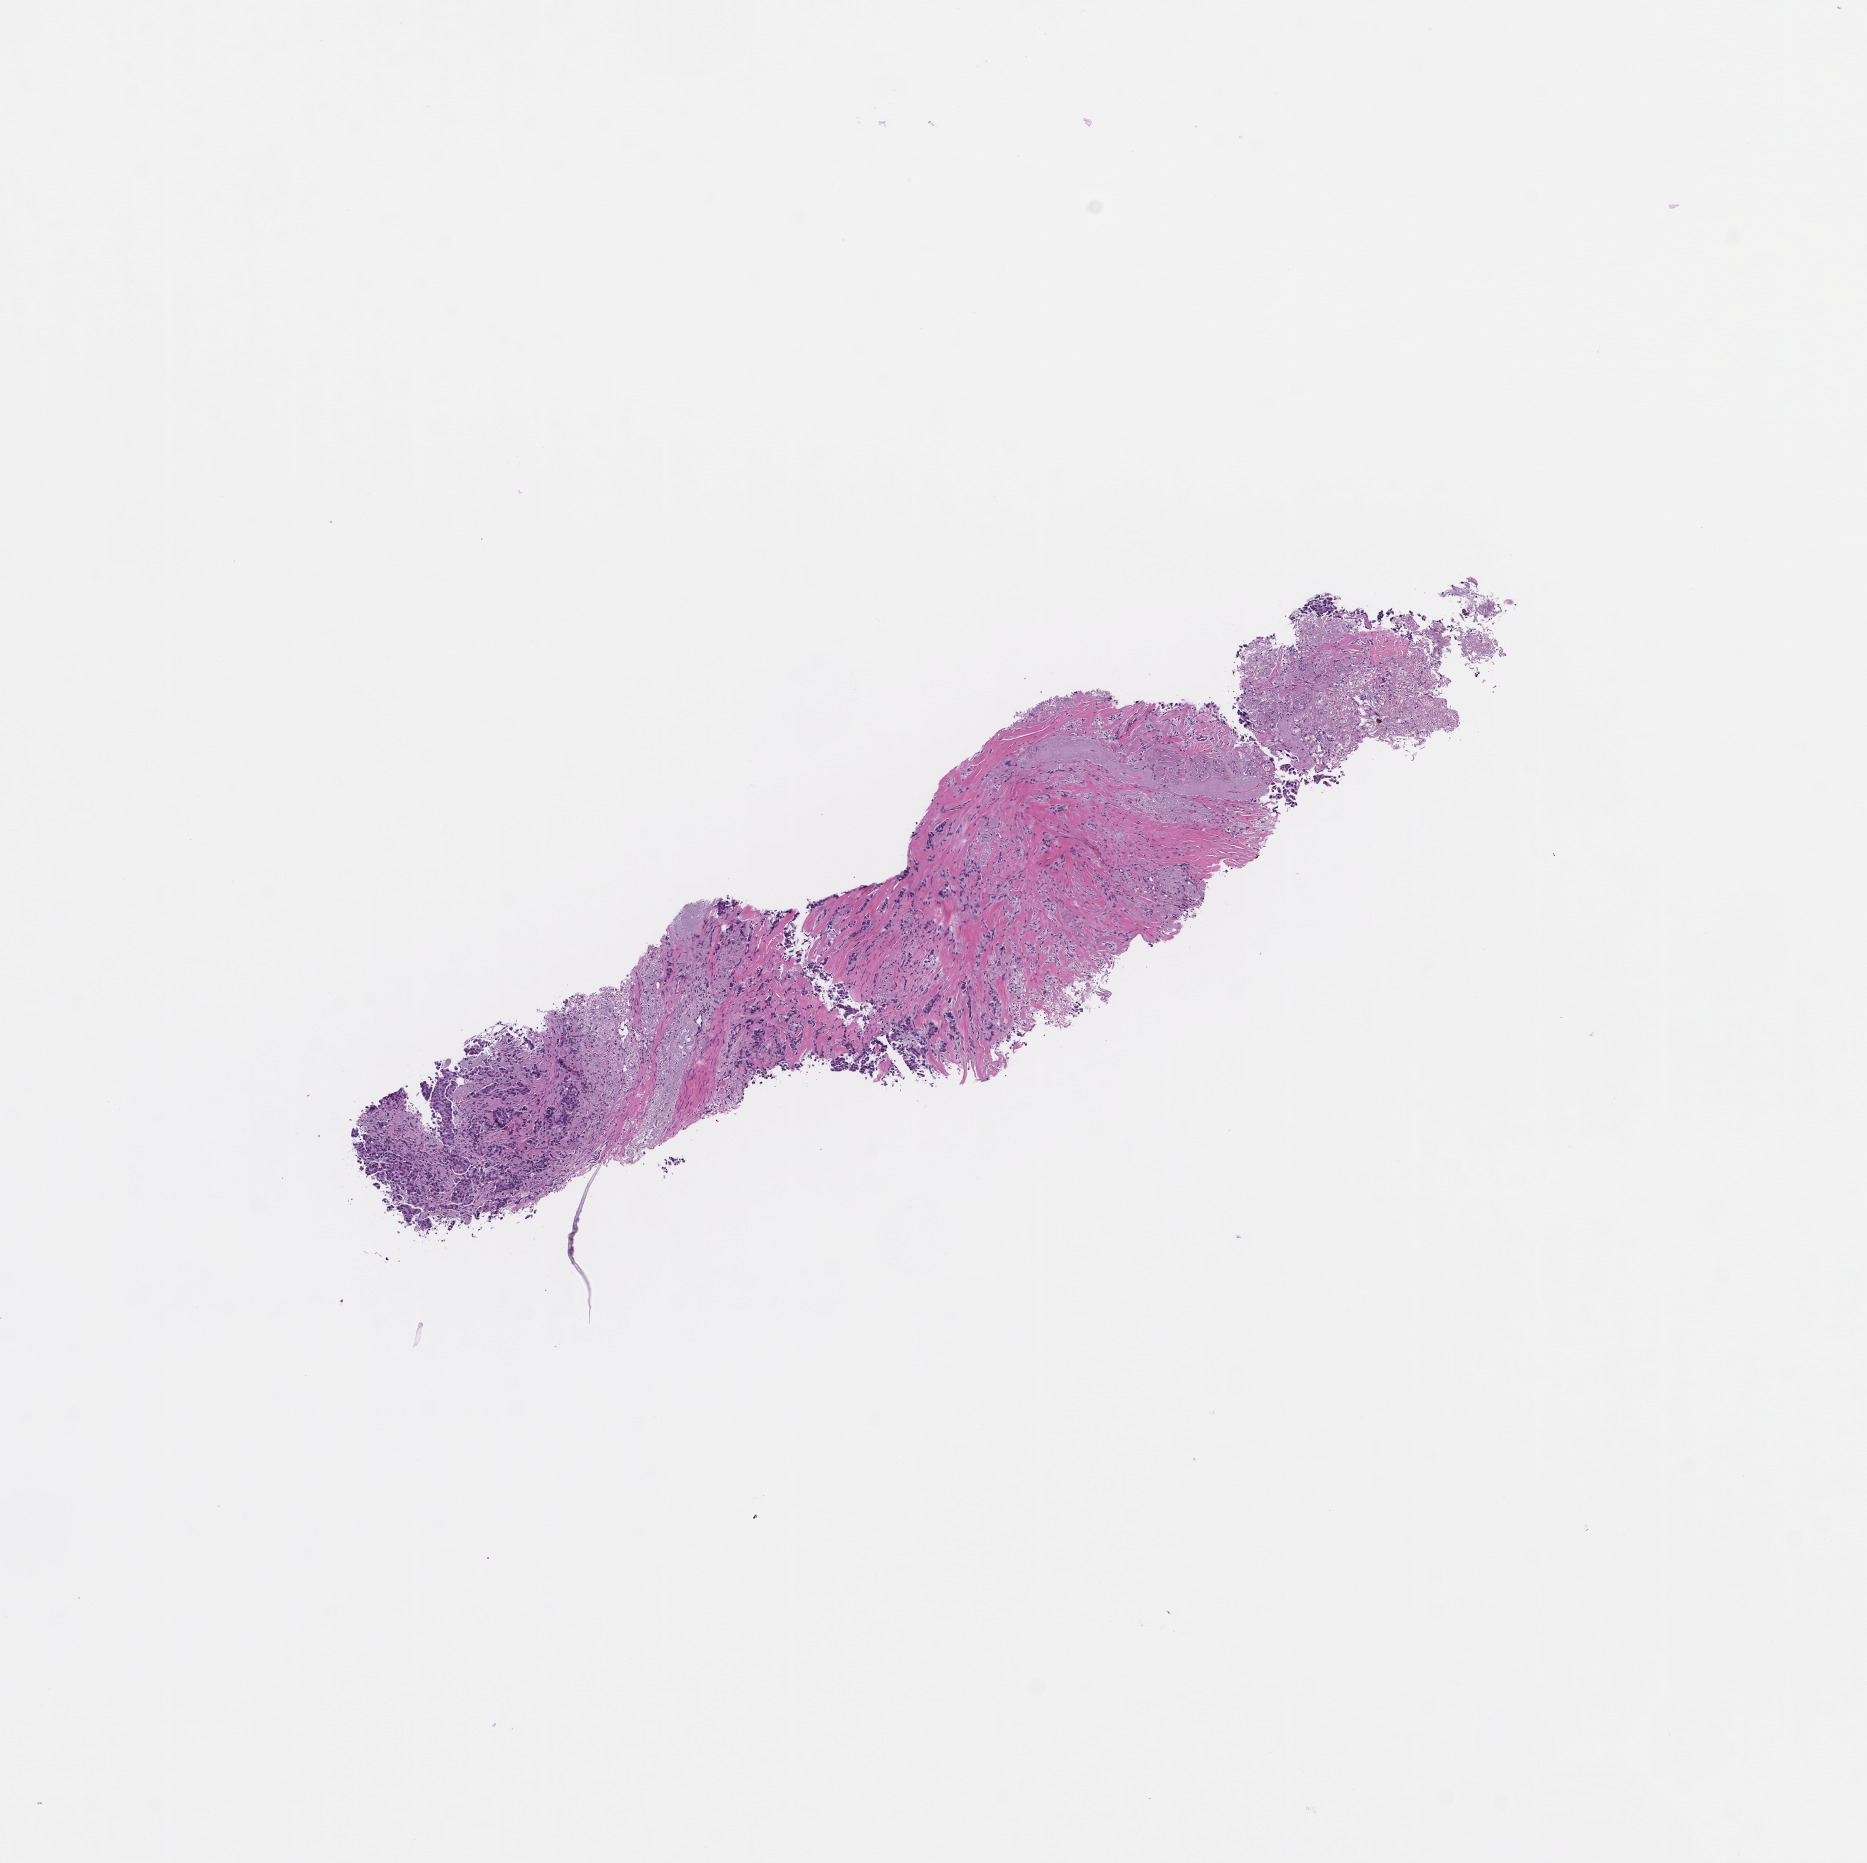
Digitized H&E-stained section, whole scanned area (about 7.5 x 7.5 mm) shown as a low-resolution overview; formalin-fixed paraffin-embedded section; site: breast; collected at baseline (before treatment). Patient sex: female.
This section: primary tumour tissue. Diagnosis: Invasive Breast Carcinoma.